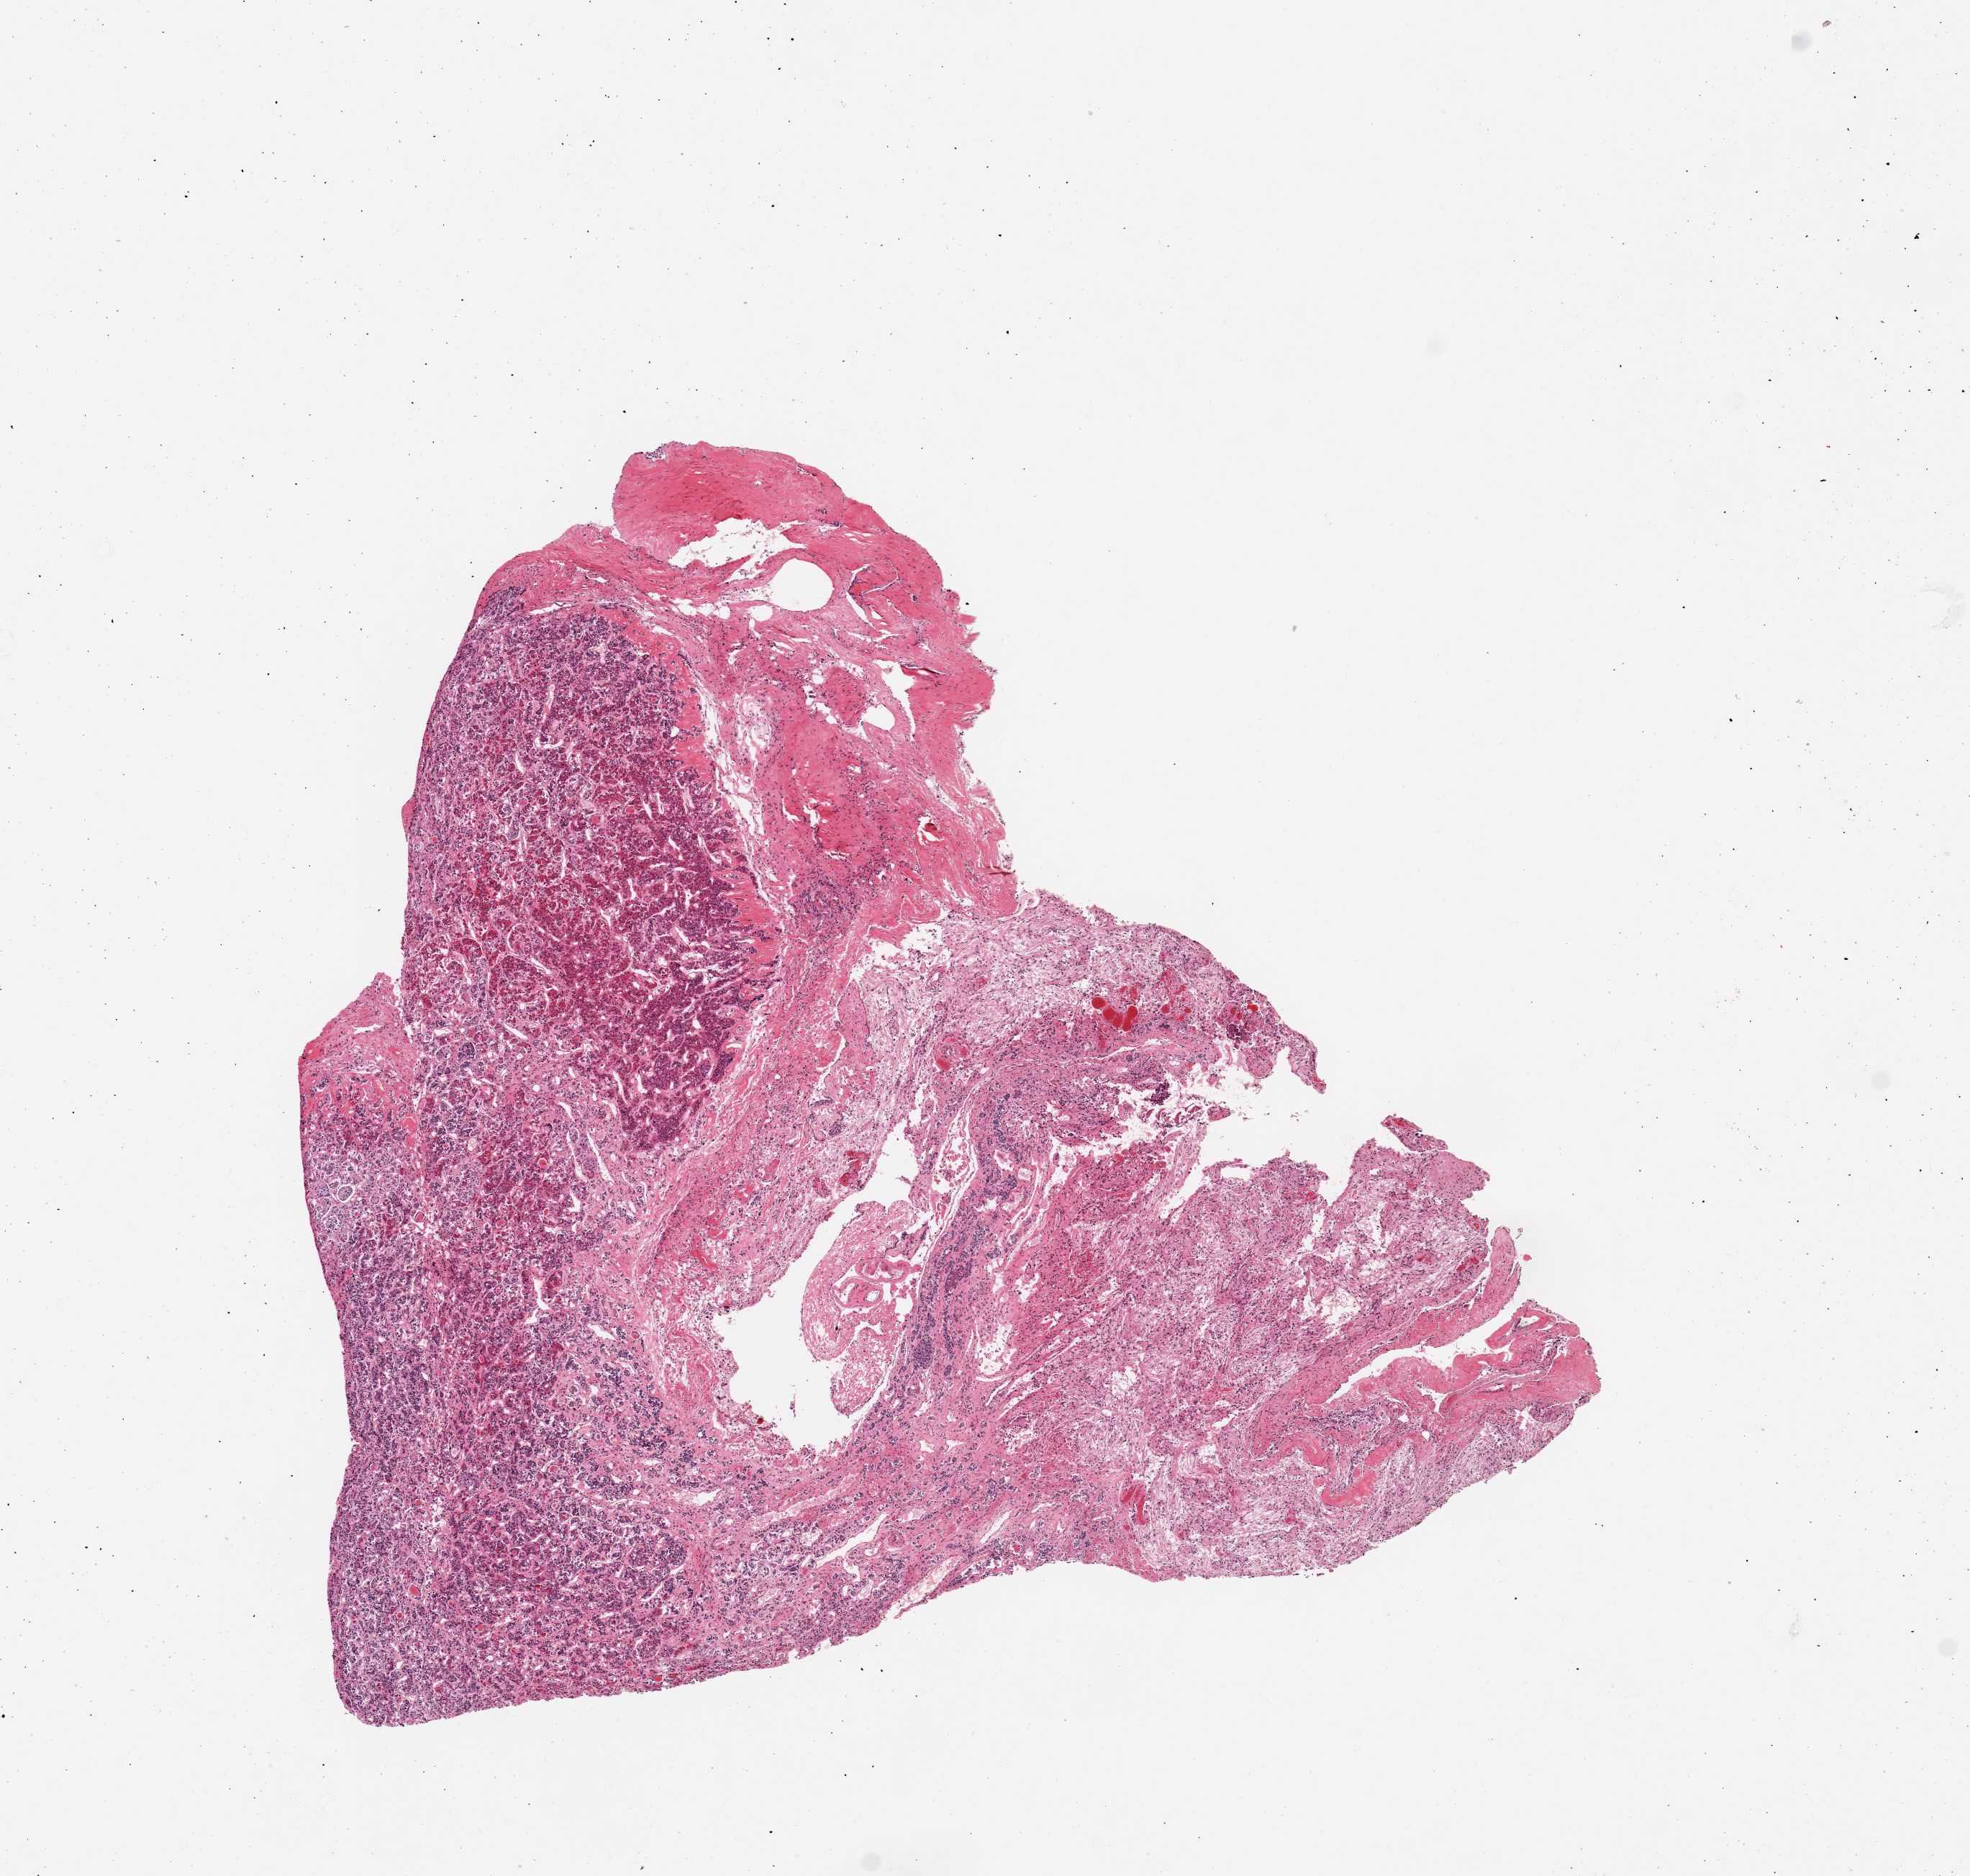
Whole-slide image, hematoxylin and eosin (H&E) stain — low-resolution overview of the scanned area, about 10.8 x 10.3 mm (acquisition: 20x scan). PAXgene-fixed paraffin-embedded (PFPE) section. Section of pituitary (target tissue). Tissue donor sample. Female donor.
Reviewer comment on this tissue sample: 1 piece; 50% fibrous stroma between anterior and posterior components.